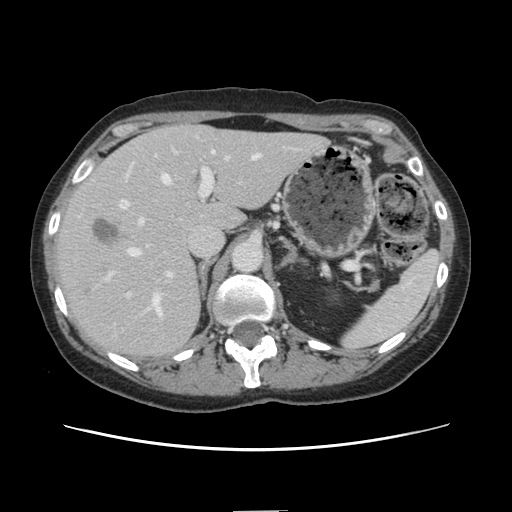
Contrast-enhanced abdominal CT, one axial slice. Soft-tissue window (W 400 / L 40 HU). 2.5 mm slice thickness. 512 × 512 image matrix, field of view 350 × 350 mm. Female patient, age 63 years. Case-level facts recorded for this patient, not image findings: diagnosis: colorectal cancer liver metastases, imaged before liver resection; multiple liver metastases: yes; largest metastasis: 3.2 cm; chemotherapy before resection: yes.
Structures marked on this image (expert manual segmentation):
- hepatic veins: bounding box <105,151,260,318> (left, top, right, bottom; pixels)
- liver: <57,126,326,358>
- planned liver remnant (the part of the liver to remain after resection): <180,126,327,231>
- portal vein (with intrahepatic branches): <119,149,232,295>